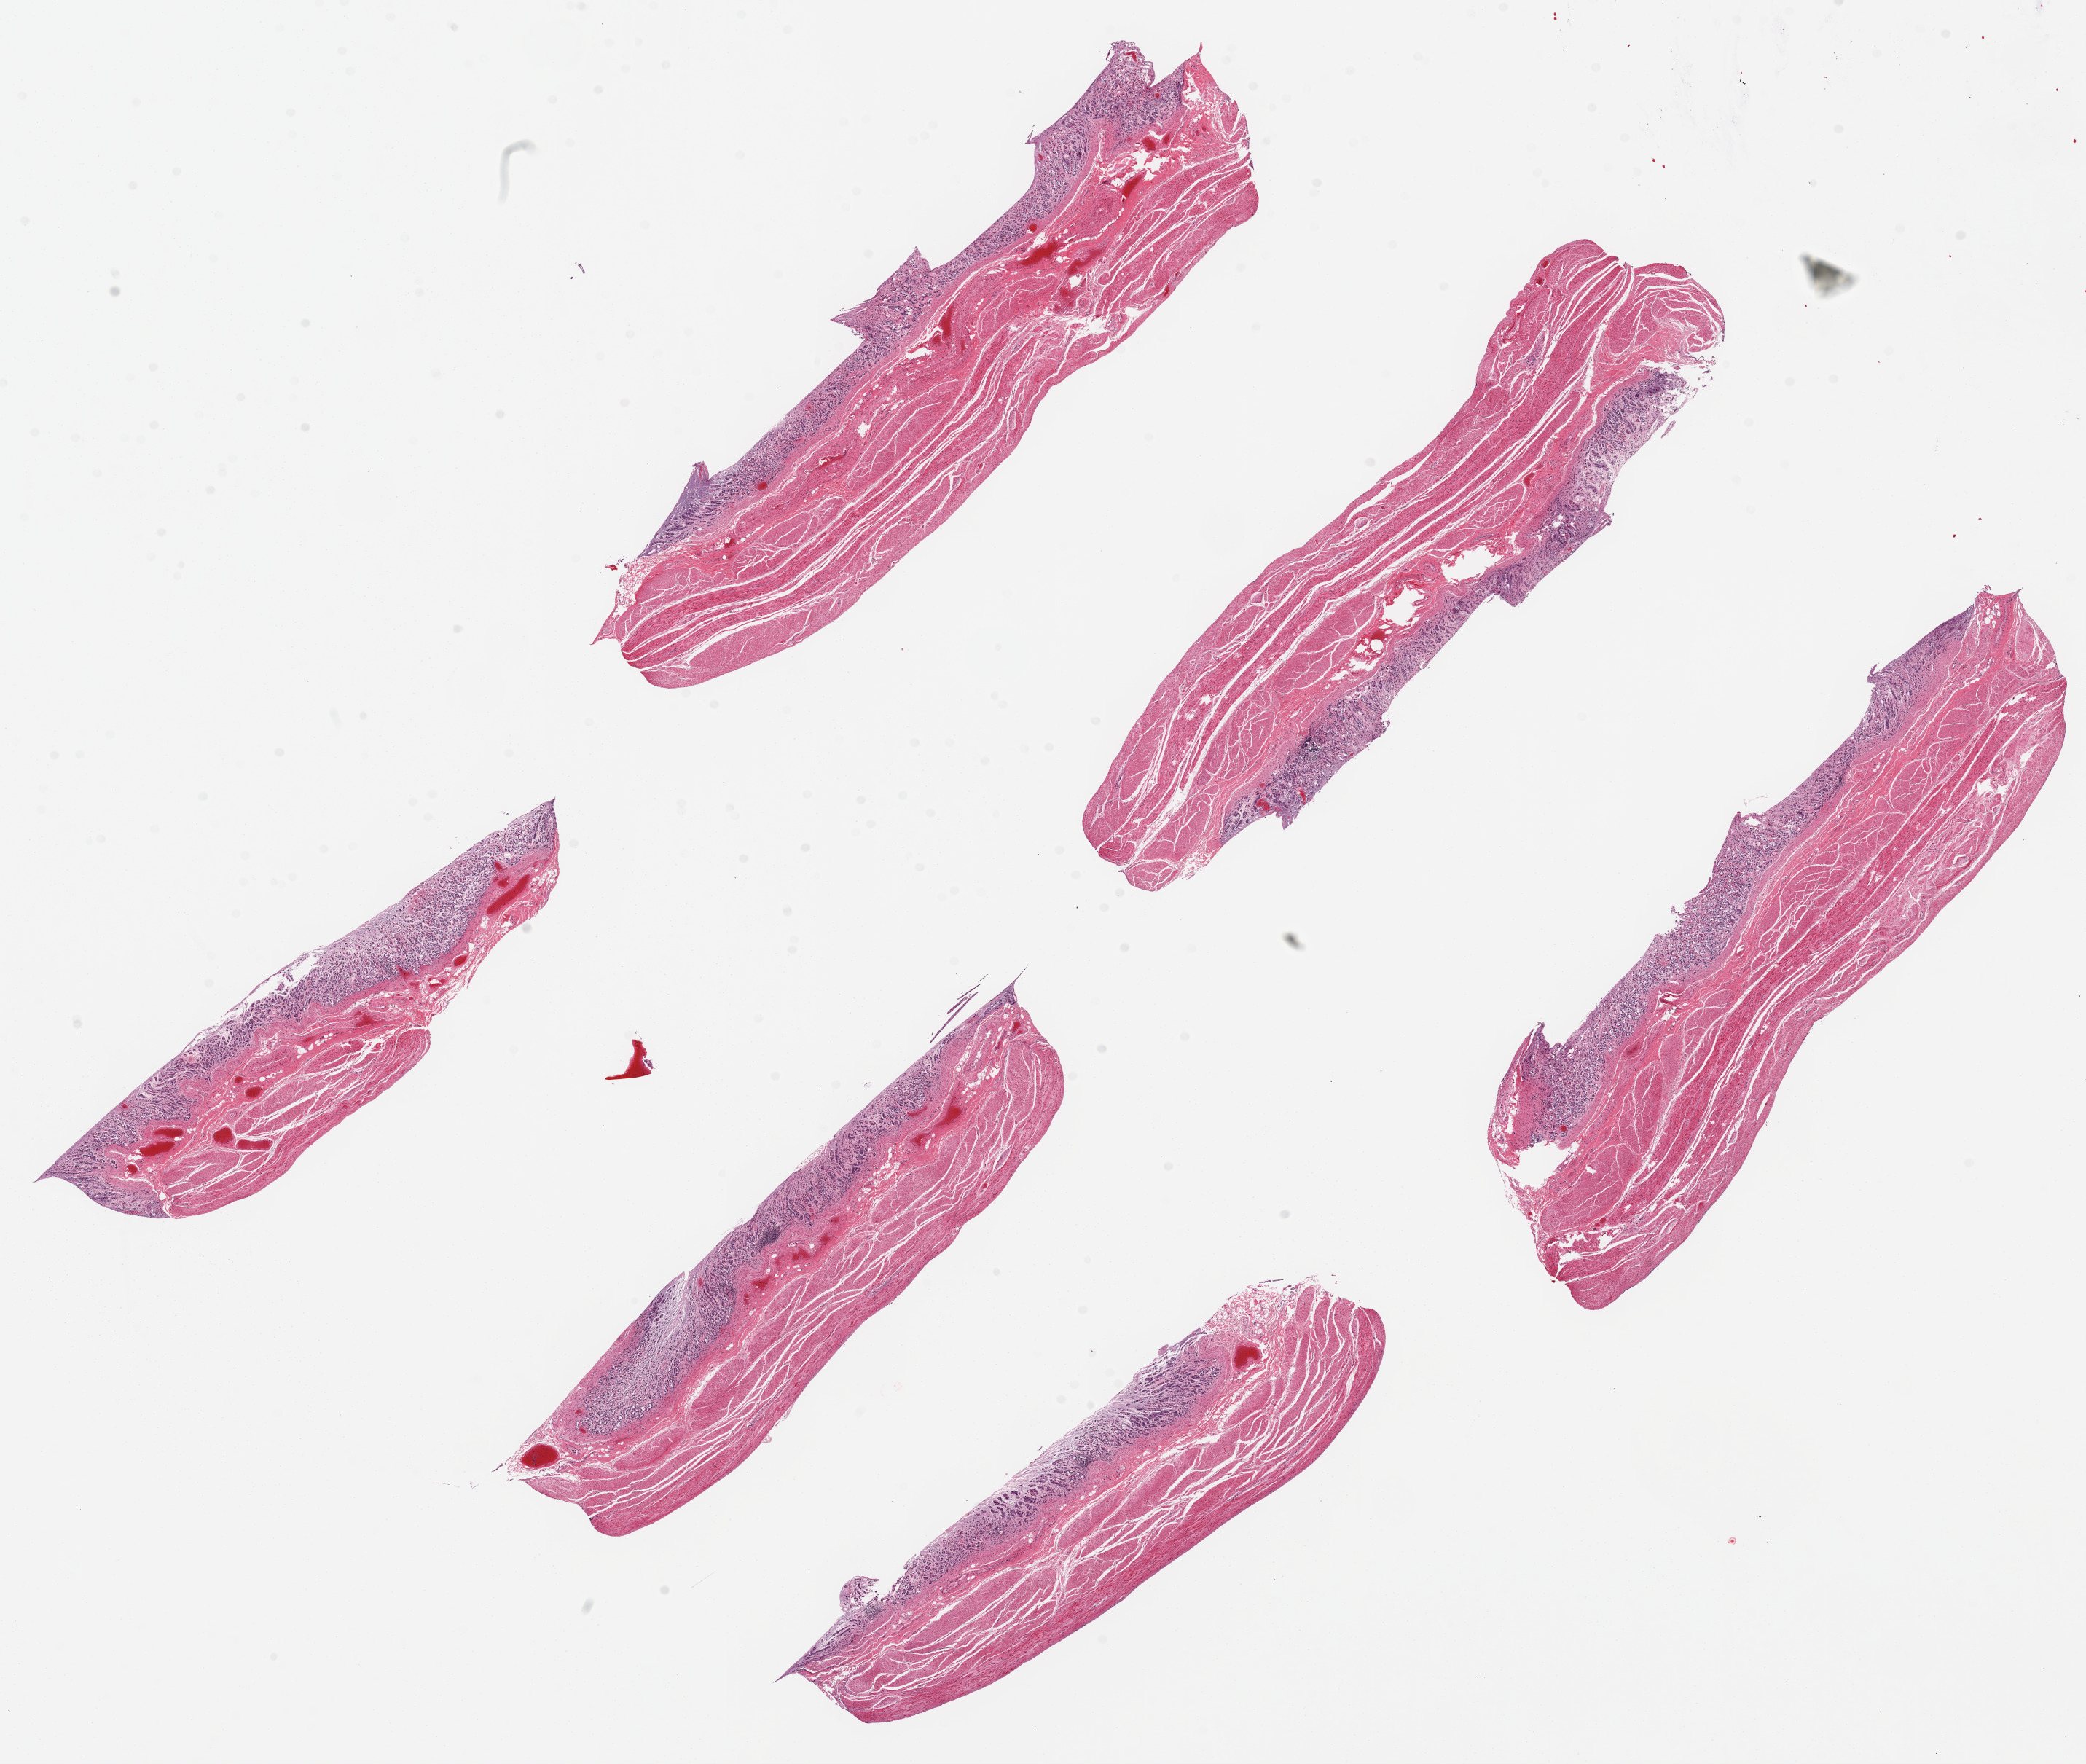
Whole-slide image, haematoxylin and eosin stain, brightfield — shown as a low-resolution overview of the whole scanned area (about 22.6 x 19.1 mm, slide scanned at 20x), PAXgene-fixed paraffin-embedded (PFPE) section, section of stomach (target tissue), tissue donor sample. Donor sex: female.
Reviewer comment on this tissue sample: 6 ~8.5x2mm pieces; mucosa nearly totally autolyzed.